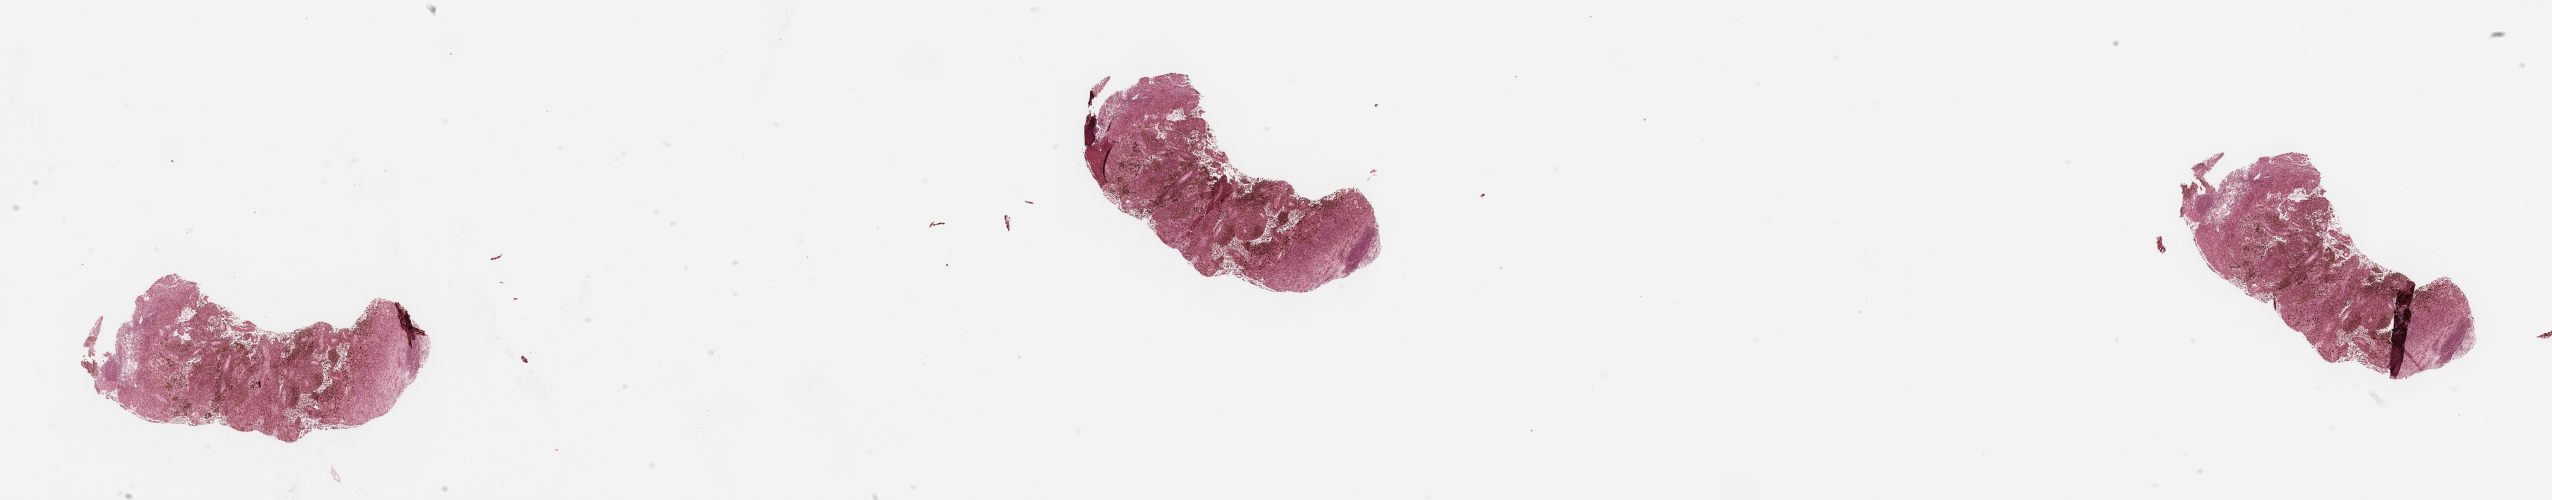
H&E whole-slide image — shown as a low-resolution overview of the whole scanned area (about 40.4 x 7.9 mm, from a 20x scan); tumour tissue sample, sampled site: lymph node. Male, 70 y/o. Slide review estimates, as recorded: tumour nuclei 90%, necrosis 0%.
This section: metastatic tumour tissue. Patient diagnosis: Malignant melanoma, NOS.